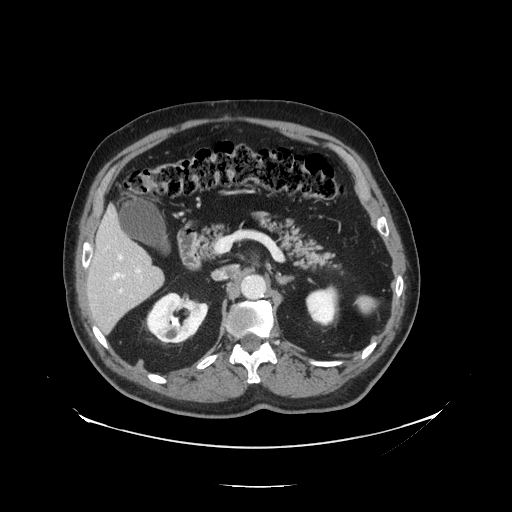
Contrast-enhanced abdominal CT, one axial slice; slice 71 of 138 in the series (ordered by position); soft-tissue window (W 400 / L 40 HU); 512 × 512 image matrix. Male patient, age 77 years. From the clinical record (not read from this slice): diagnosis: colorectal cancer liver metastases, imaged before liver resection; multiple liver metastases: no; largest metastasis: 1.5 cm; disease in both lobes: no.
Annotated regions visible in this slice (expert manual segmentation):
- hepatic veins: bounding box (x1, y1, x2, y2) in pixels: (112, 255, 124, 280)
- liver: (87, 212, 163, 334)
- planned liver remnant (the part of the liver to remain after resection): (88, 211, 153, 287)
- portal vein (with intrahepatic branches): (118, 268, 142, 293)